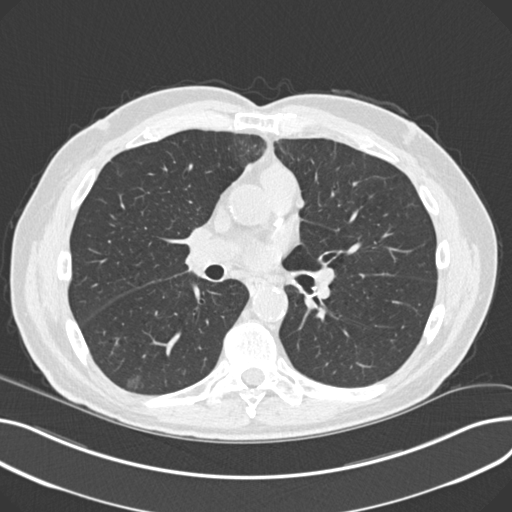
Low-dose screening chest CT, one axial slice; position 118 of 230 along the scan axis; reconstruction kernel B30f; 120 kVp; lung window (W 1500 / L -600 HU); 2 mm slice thickness; 512 × 512 image matrix, field of view 372 × 372 mm.
Outlined on this slice (expert manual segmentation):
- lesion 1 (nodule, lower lobe of right lung): bounding box [x1, y1, x2, y2] px = [127, 374, 140, 389]